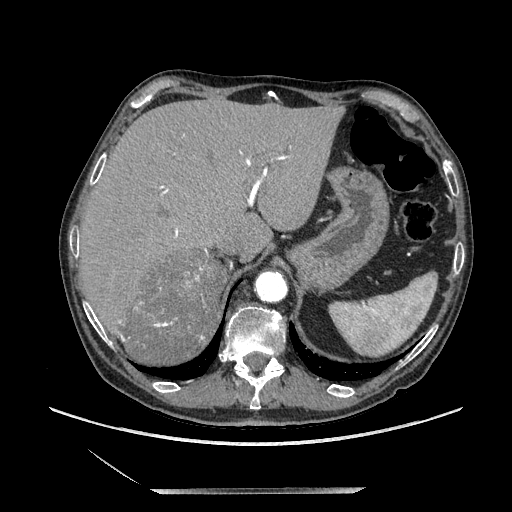
Contrast-enhanced abdominal CT, one axial slice; slice 164 of 243 in the series (ordered by position); soft-tissue window (W 400 / L 40 HU); 1.25 mm slice thickness; 512 × 512 image matrix, field of view 420 × 420 mm. Male patient. From the clinical record (not read from this slice): diagnosis: adrenocortical carcinoma; tumour side: right adrenal; tumour size at pathology: 16 cm; Ki-67 index: 17 %.
Structures marked on this image (semi-automatic segmentation, software-assisted and operator-edited):
- mass: box from (x=129, y=255) to (x=223, y=365) px